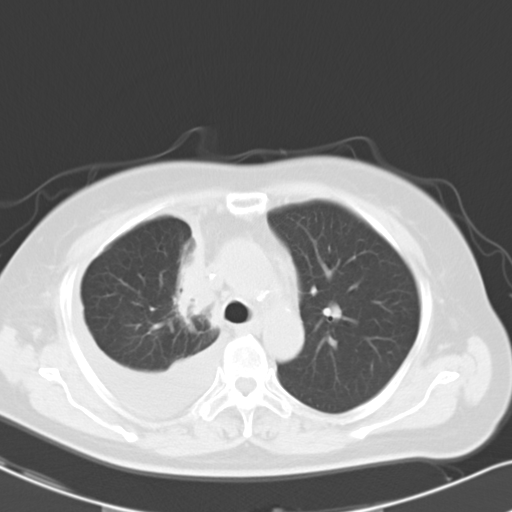
Chest CT, one axial slice. Position 19 of 26 along the scan axis. Reconstruction kernel B40f. Lung window (W 1500 / L -600 HU). 10 mm slice thickness. 512 × 512 image matrix, field of view 328 × 328 mm. Patient: female, 69 years. From the clinical record (not read from this slice): clinical TNM (as recorded): T2a N0 M1c.
Outlined on this slice (bounding box drawn by a radiologist):
- lung tumour (recorded histology: adenocarcinoma): bounding box (x1, y1, x2, y2) in pixels: (171, 215, 217, 325)